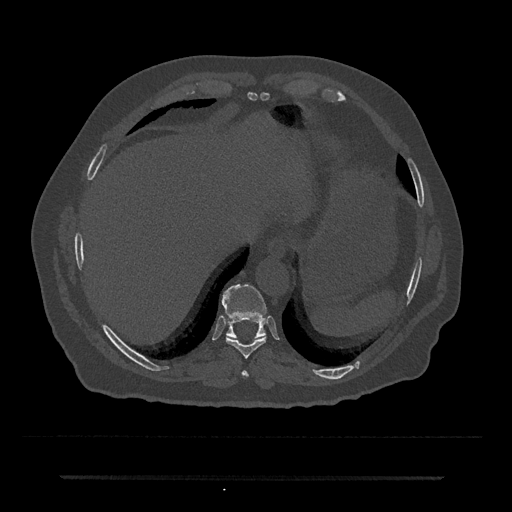
CT including the spine, one axial slice; position 261 of 797 along the scan axis; reconstruction kernel Br40s/3; bone window (W 1800 / L 400 HU); 0.5 mm slice thickness; 512 × 512 image matrix. Patient: male, 69 years. Case-level facts recorded for this patient, not image findings: primary cancer: prostate.
Outlined on this slice (semi-automatically segmented with operator editing):
- T10 vertebra: bounding box <221,284,267,338> (left, top, right, bottom; pixels)
- T8 vertebra: <242,371,248,377>
- T9 vertebra: <226,336,266,358>